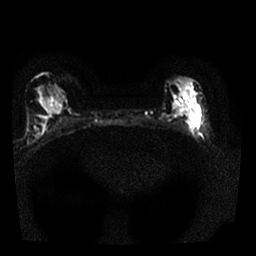
Breast MRI, one axial slice; slice 13 of 25 in the series (ordered by position); diffusion-weighted series; image 2 of 4 stored at this slice position (different b-values; order by instance number); 1.5 T; 4 mm slice thickness; 256 × 256 image matrix. Female patient.
Annotated regions visible in this slice (expert manual segmentation):
- tumour on diffusion-weighted imaging: bounding box [x1, y1, x2, y2] px = [189, 117, 198, 132]